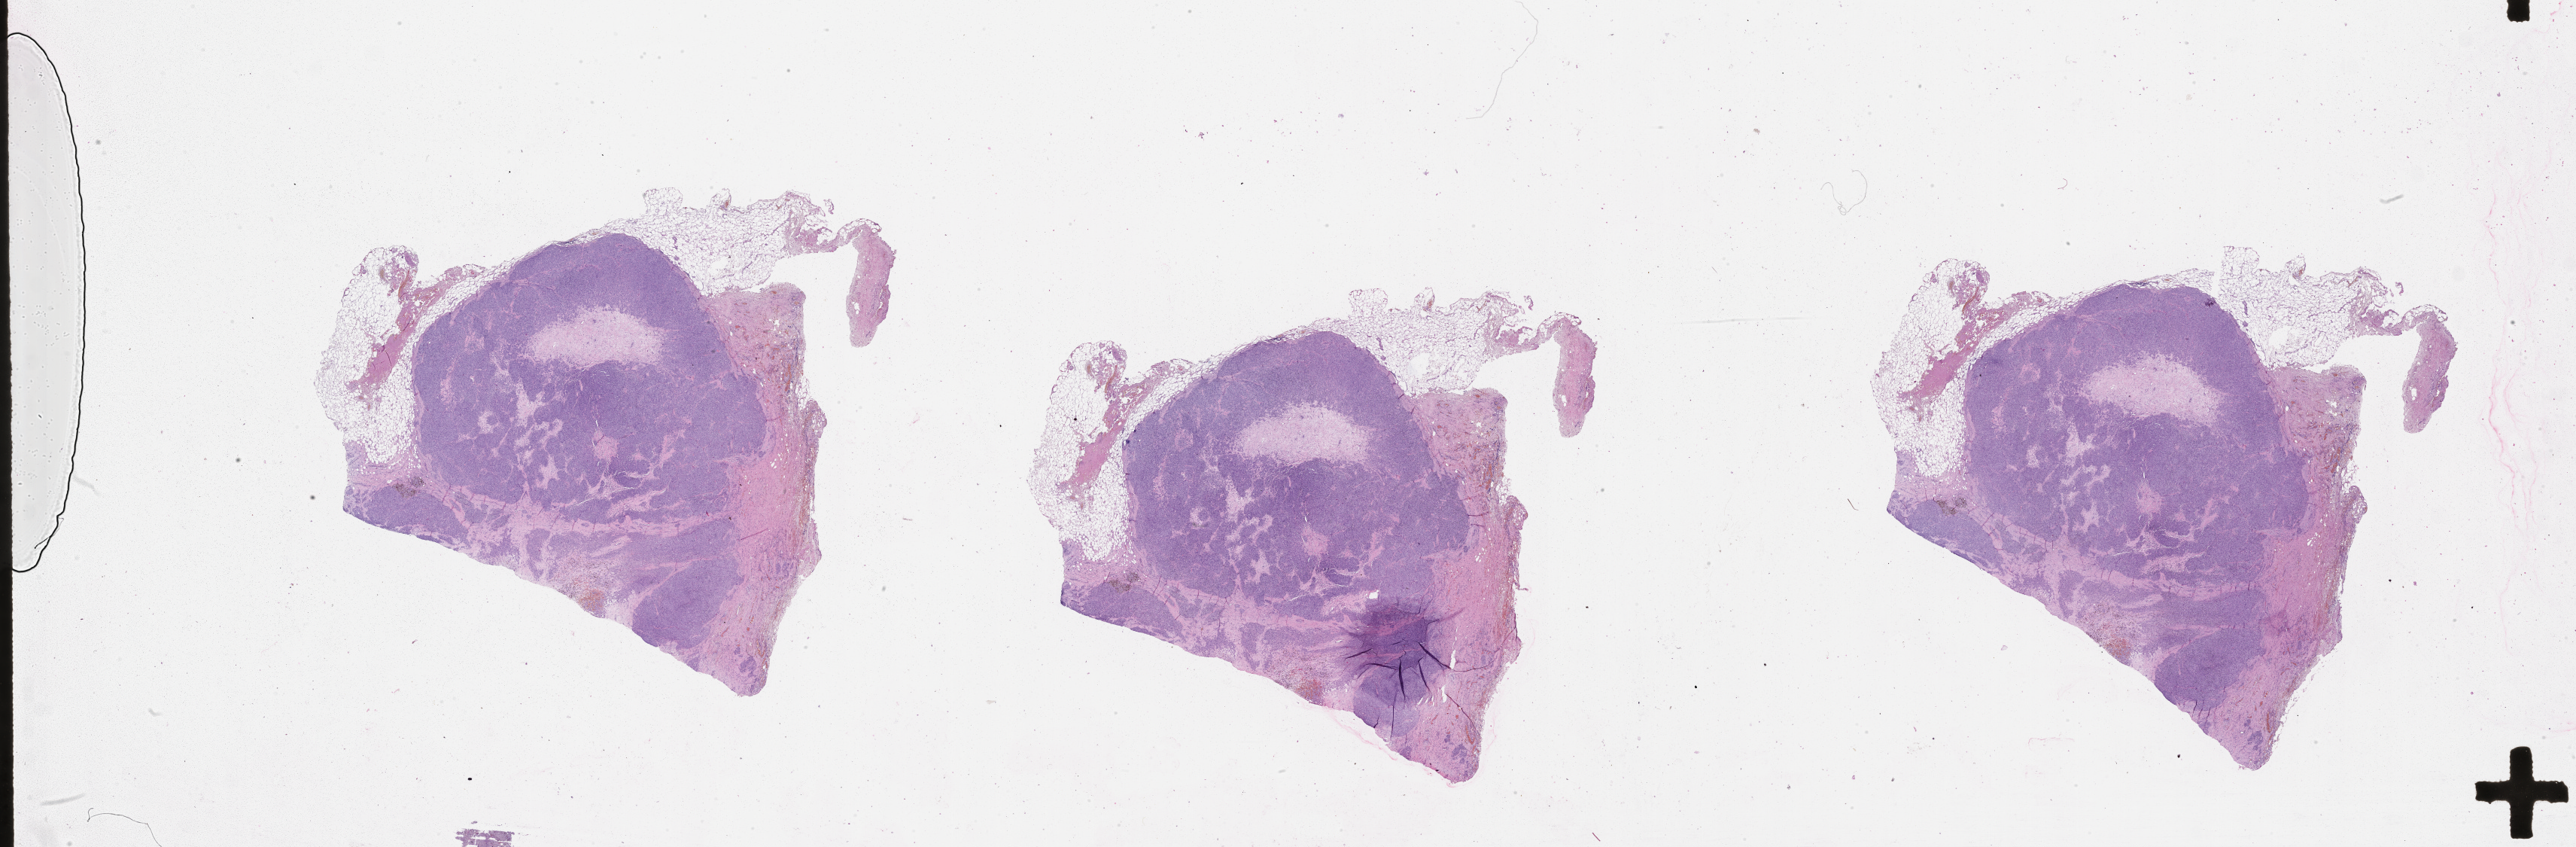
Hematoxylin and eosin (H&E) stained whole-slide image — a low-resolution overview of the entire scanned area, about 55.1 x 18.1 mm (from a 20x scan), tumour tissue sample, sampled site: lymph node. Male, 83 y/o.
This section: metastatic tumour tissue. Patient diagnosis: Malignant melanoma, NOS.